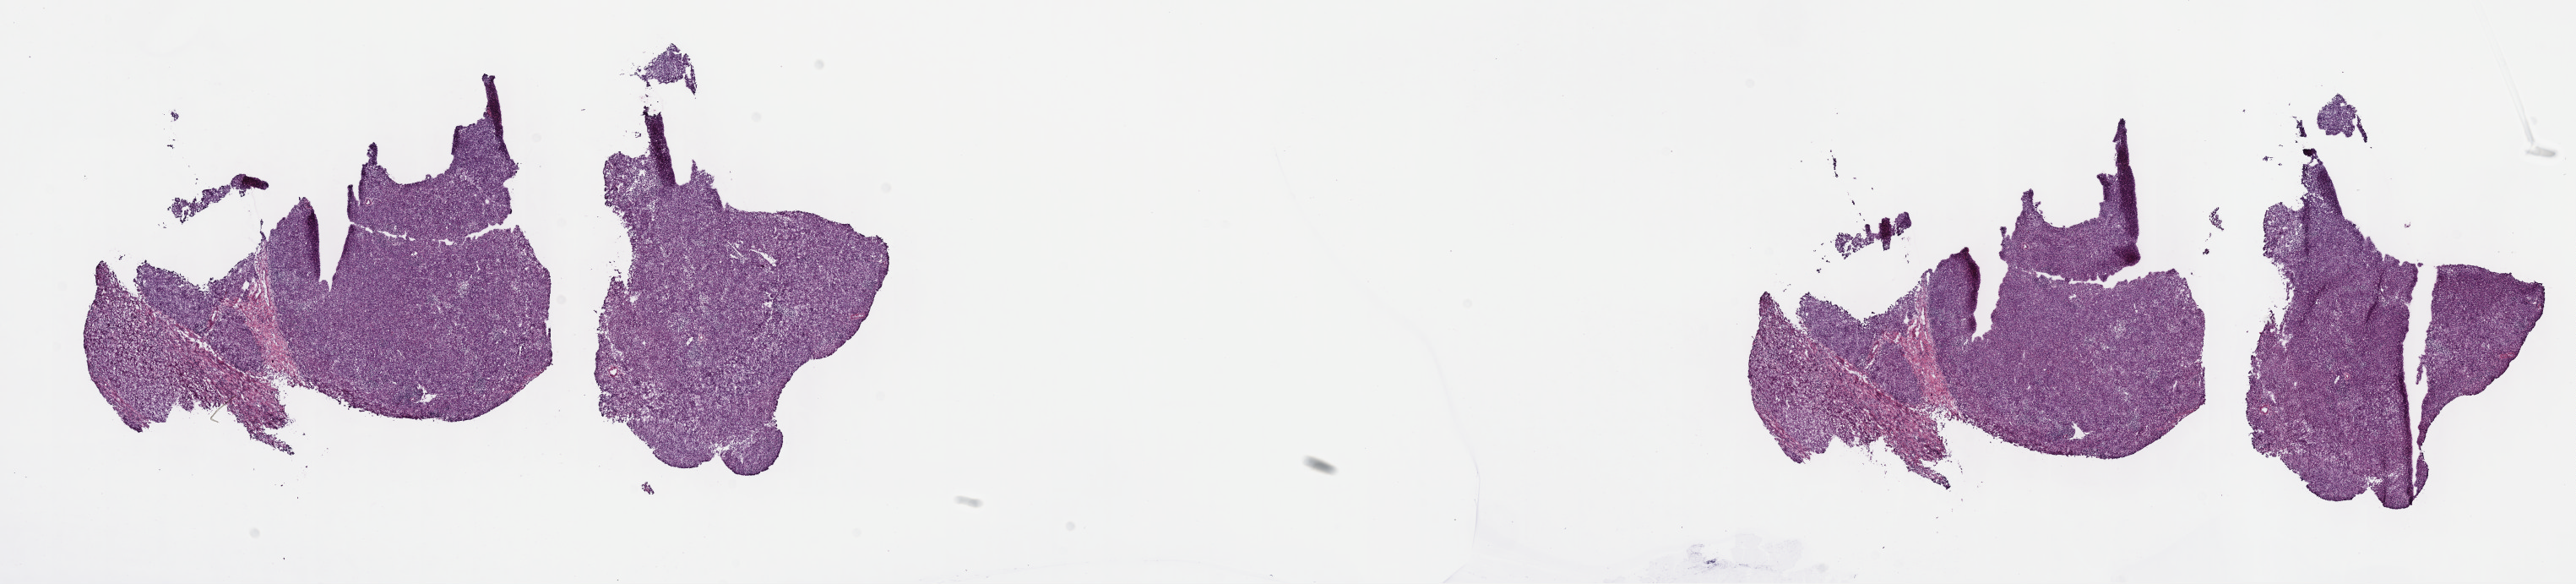
Whole-slide histology image, H&E-stained — low-resolution overview of the scanned area, about 24.7 x 5.6 mm (from a 40x scan), frozen section, primary tumour sample from the liver. Male, age 61 years at initial diagnosis. Histologic grade: G2 (moderately differentiated). Composition of this section per pathologist review: tumour cells 78%, tumour nuclei 78%, normal cells 0%, stromal cells 20%, necrosis 2%. Infiltration values recorded for this section: lymphocyte infiltration 22%, monocyte infiltration 1%, neutrophil infiltration 2%.
TNM: T1 N0 M0. AJCC pathologic stage: I (6th edition). Diagnosis: Combined hepatocellular carcinoma and cholangiocarcinoma.